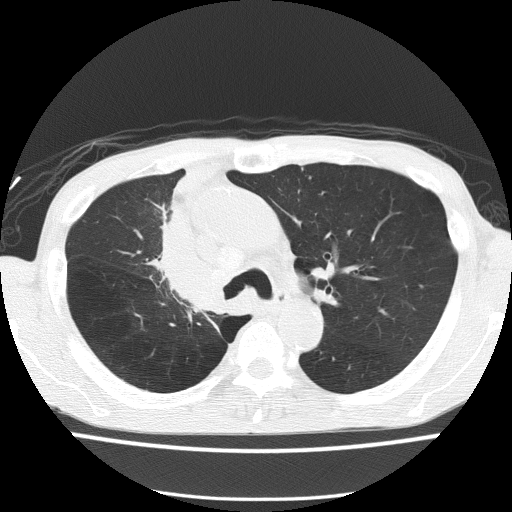
Low-dose screening chest CT, one axial slice. Position 101 of 150 along the scan axis. Lung window (W 1500 / L -600 HU). 2 mm slice thickness. 512 × 512 image matrix, field of view 336 × 336 mm.
Structures marked on this image (outlined manually by an expert reader):
- lesion 1 (tumor, hilum of right lung): bounding box (x1, y1, x2, y2) in pixels: (162, 212, 225, 309)